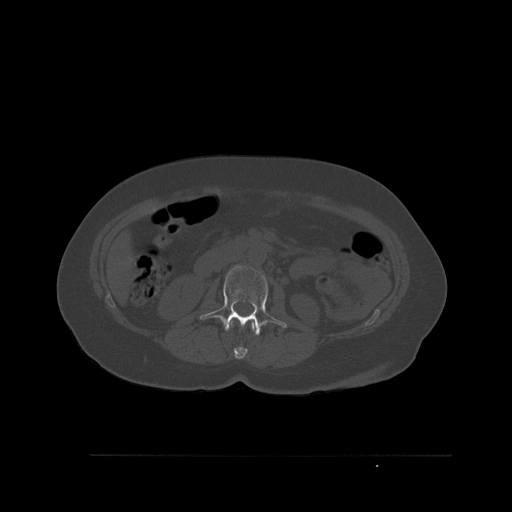
CT including the spine, one axial slice; position 247 of 527 along the scan axis; bone window (W 1800 / L 400 HU); 512 × 512 image matrix, field of view 470 × 470 mm. Female patient, age 73 years. Case-level facts recorded for this patient, not image findings: primary cancer: breast; vertebrae with lytic lesions (as recorded): L2.
Outlined on this slice (semi-automatic segmentation, software-assisted and operator-edited):
- L1 vertebra: bounding box [x1, y1, x2, y2] px = [230, 320, 255, 359]
- L2 vertebra: [200, 264, 287, 336]